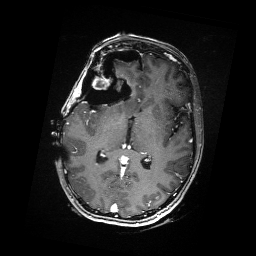
Brain MRI from a brain-tumour surgery series, one axial slice; slice 91 of 176 in the series (ordered by position); T1-weighted post-contrast; 1 mm slice thickness; 256 × 256 image matrix, field of view 256 × 256 mm. Case-level facts recorded for this patient, not image findings: histopathology: Metastatic Carcinoma from Breast primary.
Annotated regions visible in this slice (outlined manually by an expert reader):
- residual tumour: box from (x=88, y=69) to (x=117, y=88) px